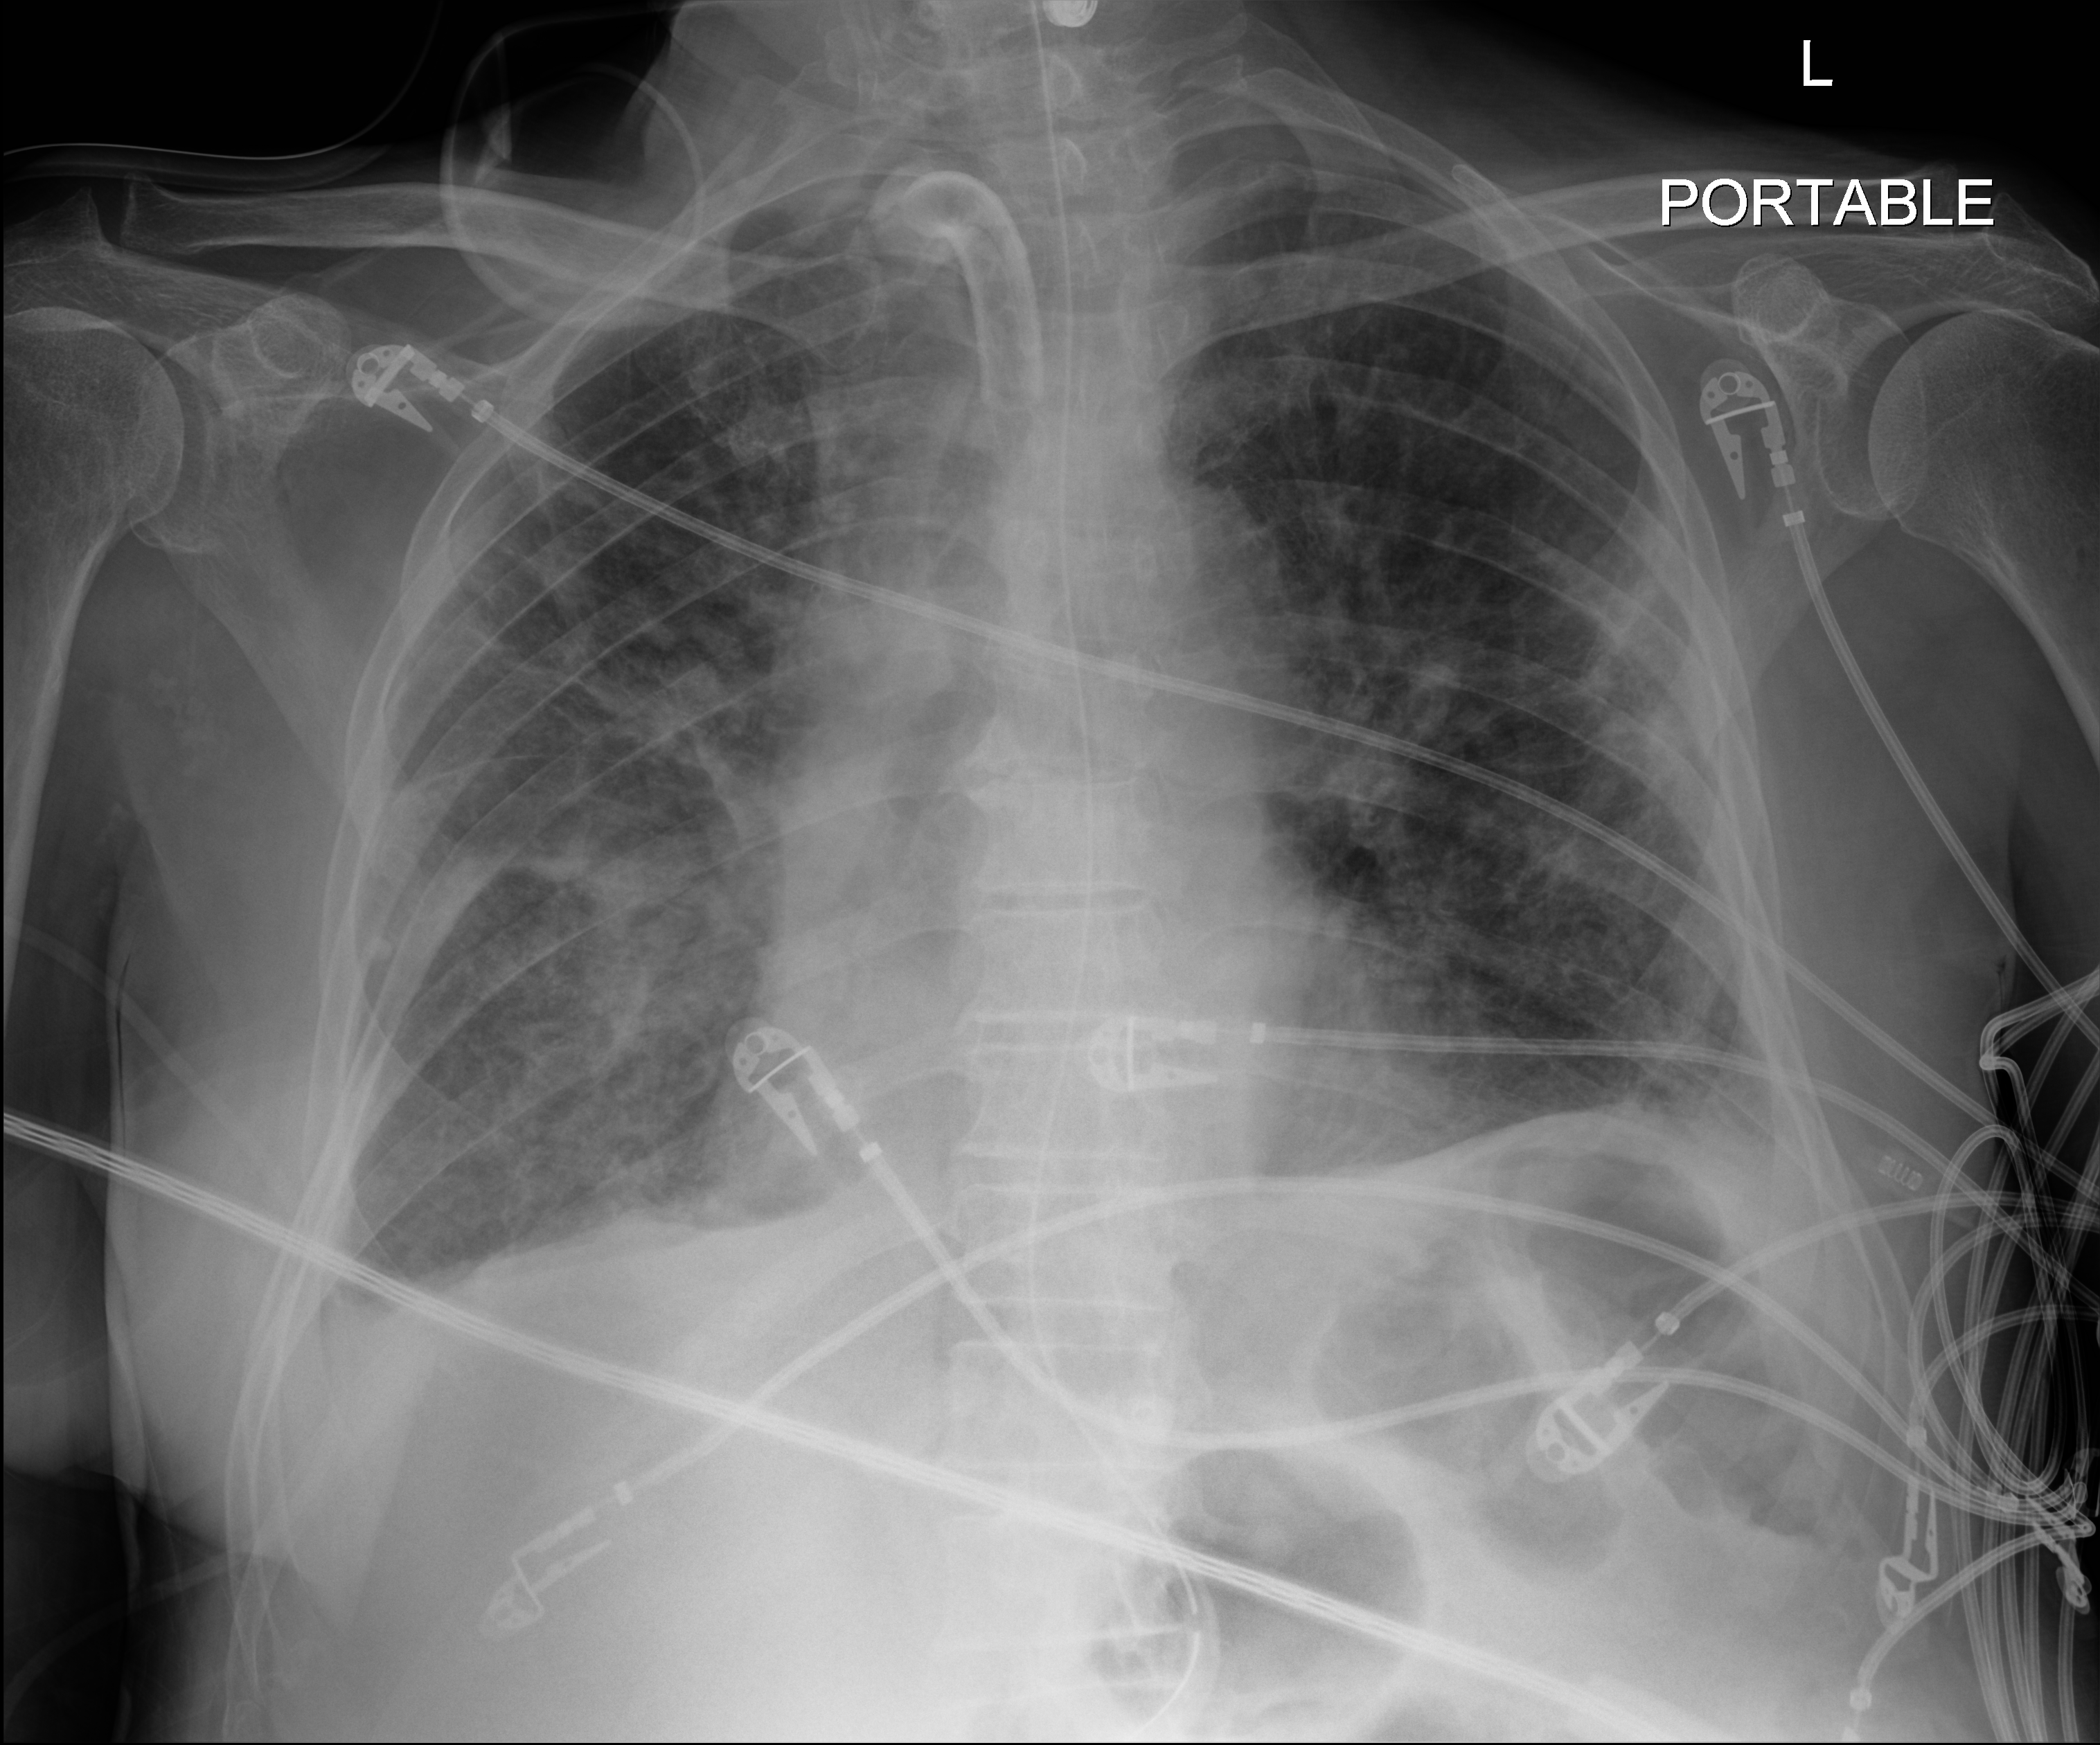
Portable chest radiograph, anteroposterior (AP) projection. Patient hospitalised with COVID-19; male, aged 75–90 years.
Hospital-stay facts (about this admission, not read from this image; timing relative to this image not recorded): smoking status (admission record): never; admitted to intensive care during this hospital stay: yes; chronic kidney disease (admission record): no.